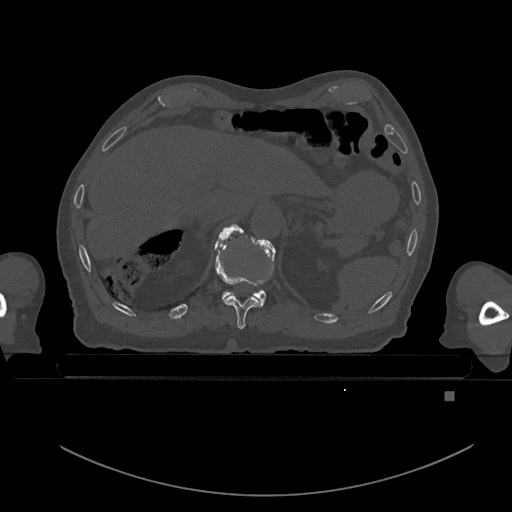
CT including the spine, one axial slice; bone window (W 1800 / L 400 HU); 512 × 512 image matrix. Male patient, age 82 years. From the clinical record (not read from this slice): primary cancer: prostate.
Outlined on this slice (semi-automatic segmentation, software-assisted and operator-edited):
- T10 vertebra: bounding box [x1, y1, x2, y2] px = [214, 225, 261, 330]
- T11 vertebra: [218, 223, 276, 306]